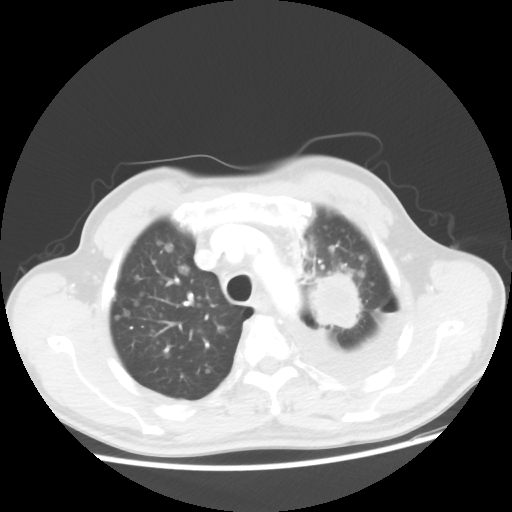
Chest CT, one axial slice. Slice 38 of 48 in the series (ordered by position). Reconstruction kernel STANDARD. 100 kVp. Lung window (W 1500 / L -600 HU). 512 × 512 image matrix, field of view 362 × 362 mm. Male patient, age 55 years. Case-level facts recorded for this patient, not image findings: clinical TNM (as recorded): T2 N3 M1a.
Structures marked on this image (bounding box drawn by a radiologist):
- lung tumour (recorded histology: squamous cell carcinoma): bounding box (x1, y1, x2, y2) in pixels: (310, 271, 364, 339)